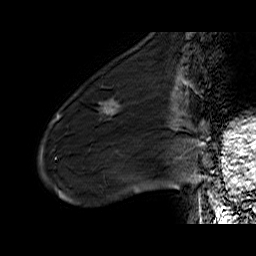
Breast MRI (dynamic contrast-enhanced), one sagittal slice; slice 18 of 60 in the series (ordered by position); dynamic contrast-enhanced series, time point 2 of 6 at this slice position (early post-contrast); 1.5 T; TE 6.5 ms, TR 32.9 ms; 4 mm slice thickness; 256 × 256 image matrix. Female patient. Case-level facts recorded for this patient, not image findings: setting: breast cancer imaged before/during neoadjuvant chemotherapy; receptor status: HER2-positive.
Structures marked on this image (semi-automatic segmentation, software-assisted and operator-edited):
- analysis volume of interest (the breast-tissue region the enhancement analysis was run in; not a lesion): box from (x=72, y=88) to (x=133, y=137) px
- tumour enhancement mask (voxels above the 100 % enhancement threshold inside the analysis volume of interest): (x=105, y=106)–(x=118, y=114)